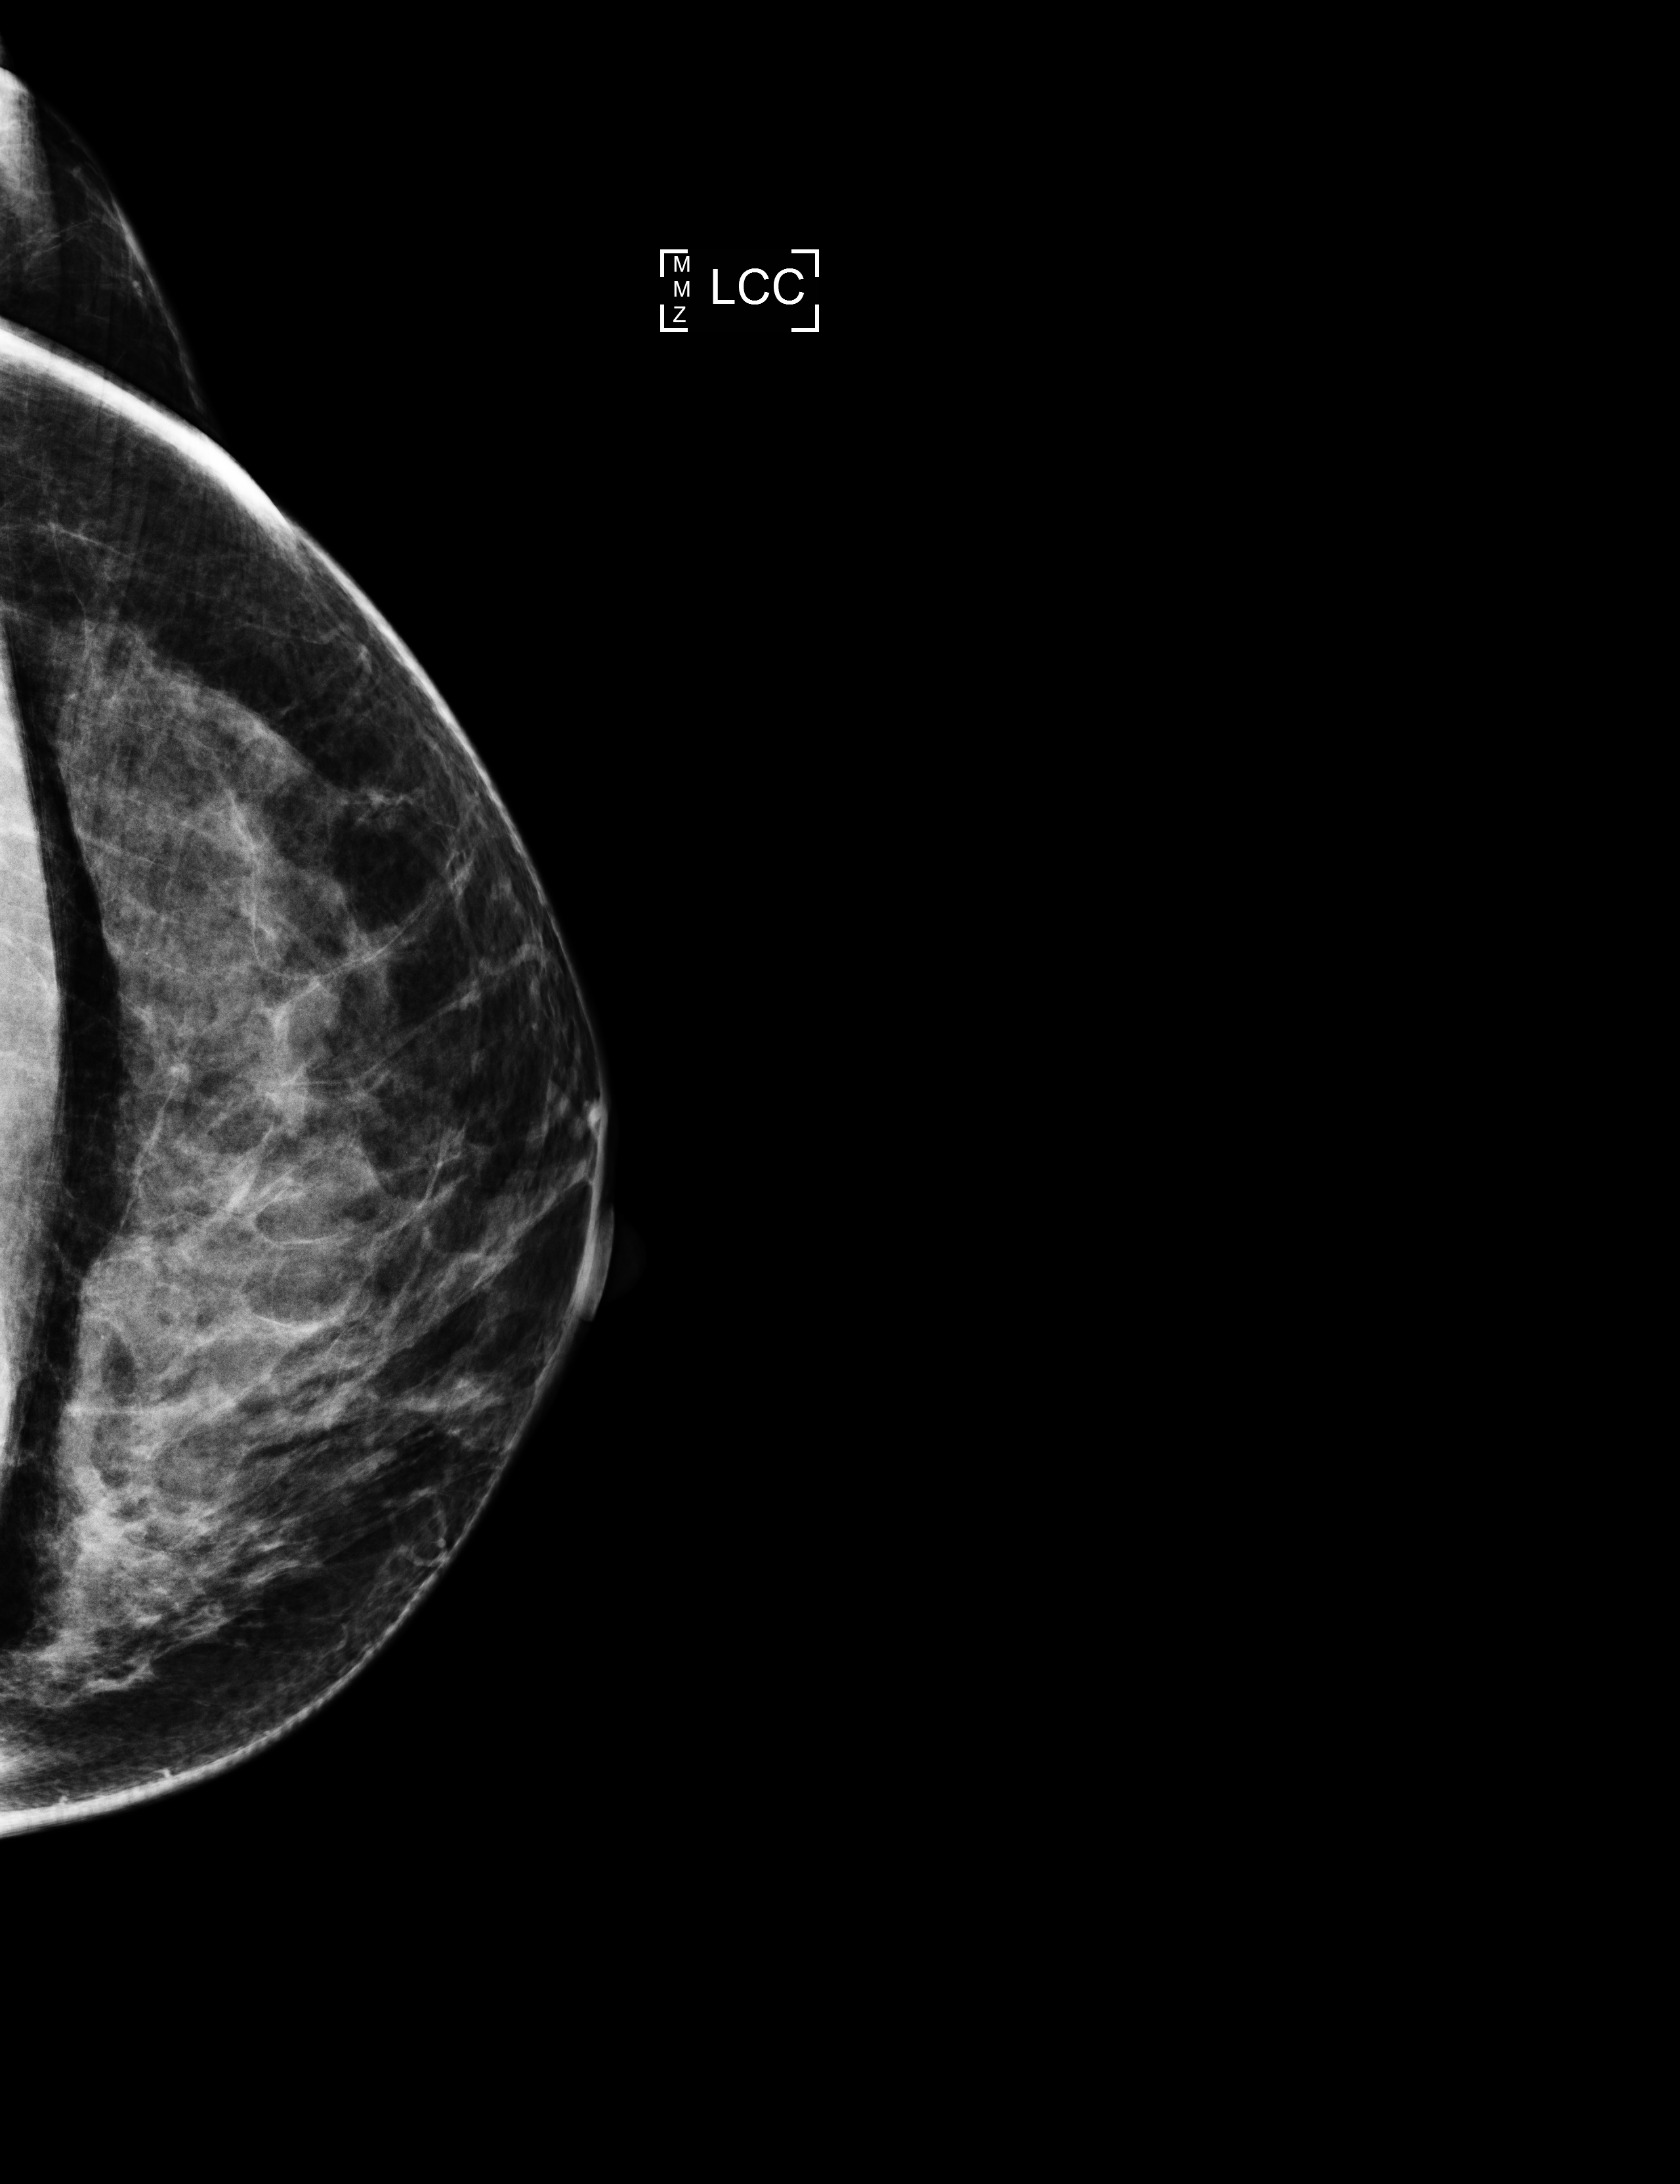
Full-field digital mammogram (FFDM); left breast; CC view; annual screening mammography examination. Female patient, age 47 years.
BI-RADS breast density category at the screening exam (both breasts, scale 1–4): 3. Final BI-RADS category for the screening round (tomosynthesis exam, both breasts): category 1. Recall: no recall after this screen.